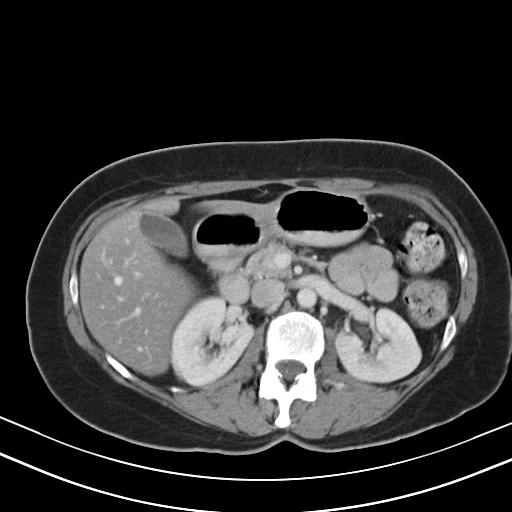
Contrast-enhanced abdominal CT, one axial slice; slice 23 of 47 in the series (ordered by position); 130 kVp; intravenous contrast given; soft-tissue window (W 400 / L 40 HU); 5 mm slice thickness; 512 × 512 image matrix, field of view 350 × 350 mm. Female patient. From the clinical record (not read from this slice): diagnosis: colorectal cancer liver metastases, imaged before liver resection; multiple liver metastases: no; largest metastasis: 3.5 cm; disease in both lobes: no.
Annotated regions visible in this slice (expert manual segmentation):
- hepatic veins: box from (x=115, y=277) to (x=139, y=313) px
- liver: (x=81, y=208)–(x=252, y=373)
- planned liver remnant (the part of the liver to remain after resection): (x=81, y=204)–(x=252, y=373)
- portal vein (with intrahepatic branches): (x=133, y=271)–(x=142, y=278)